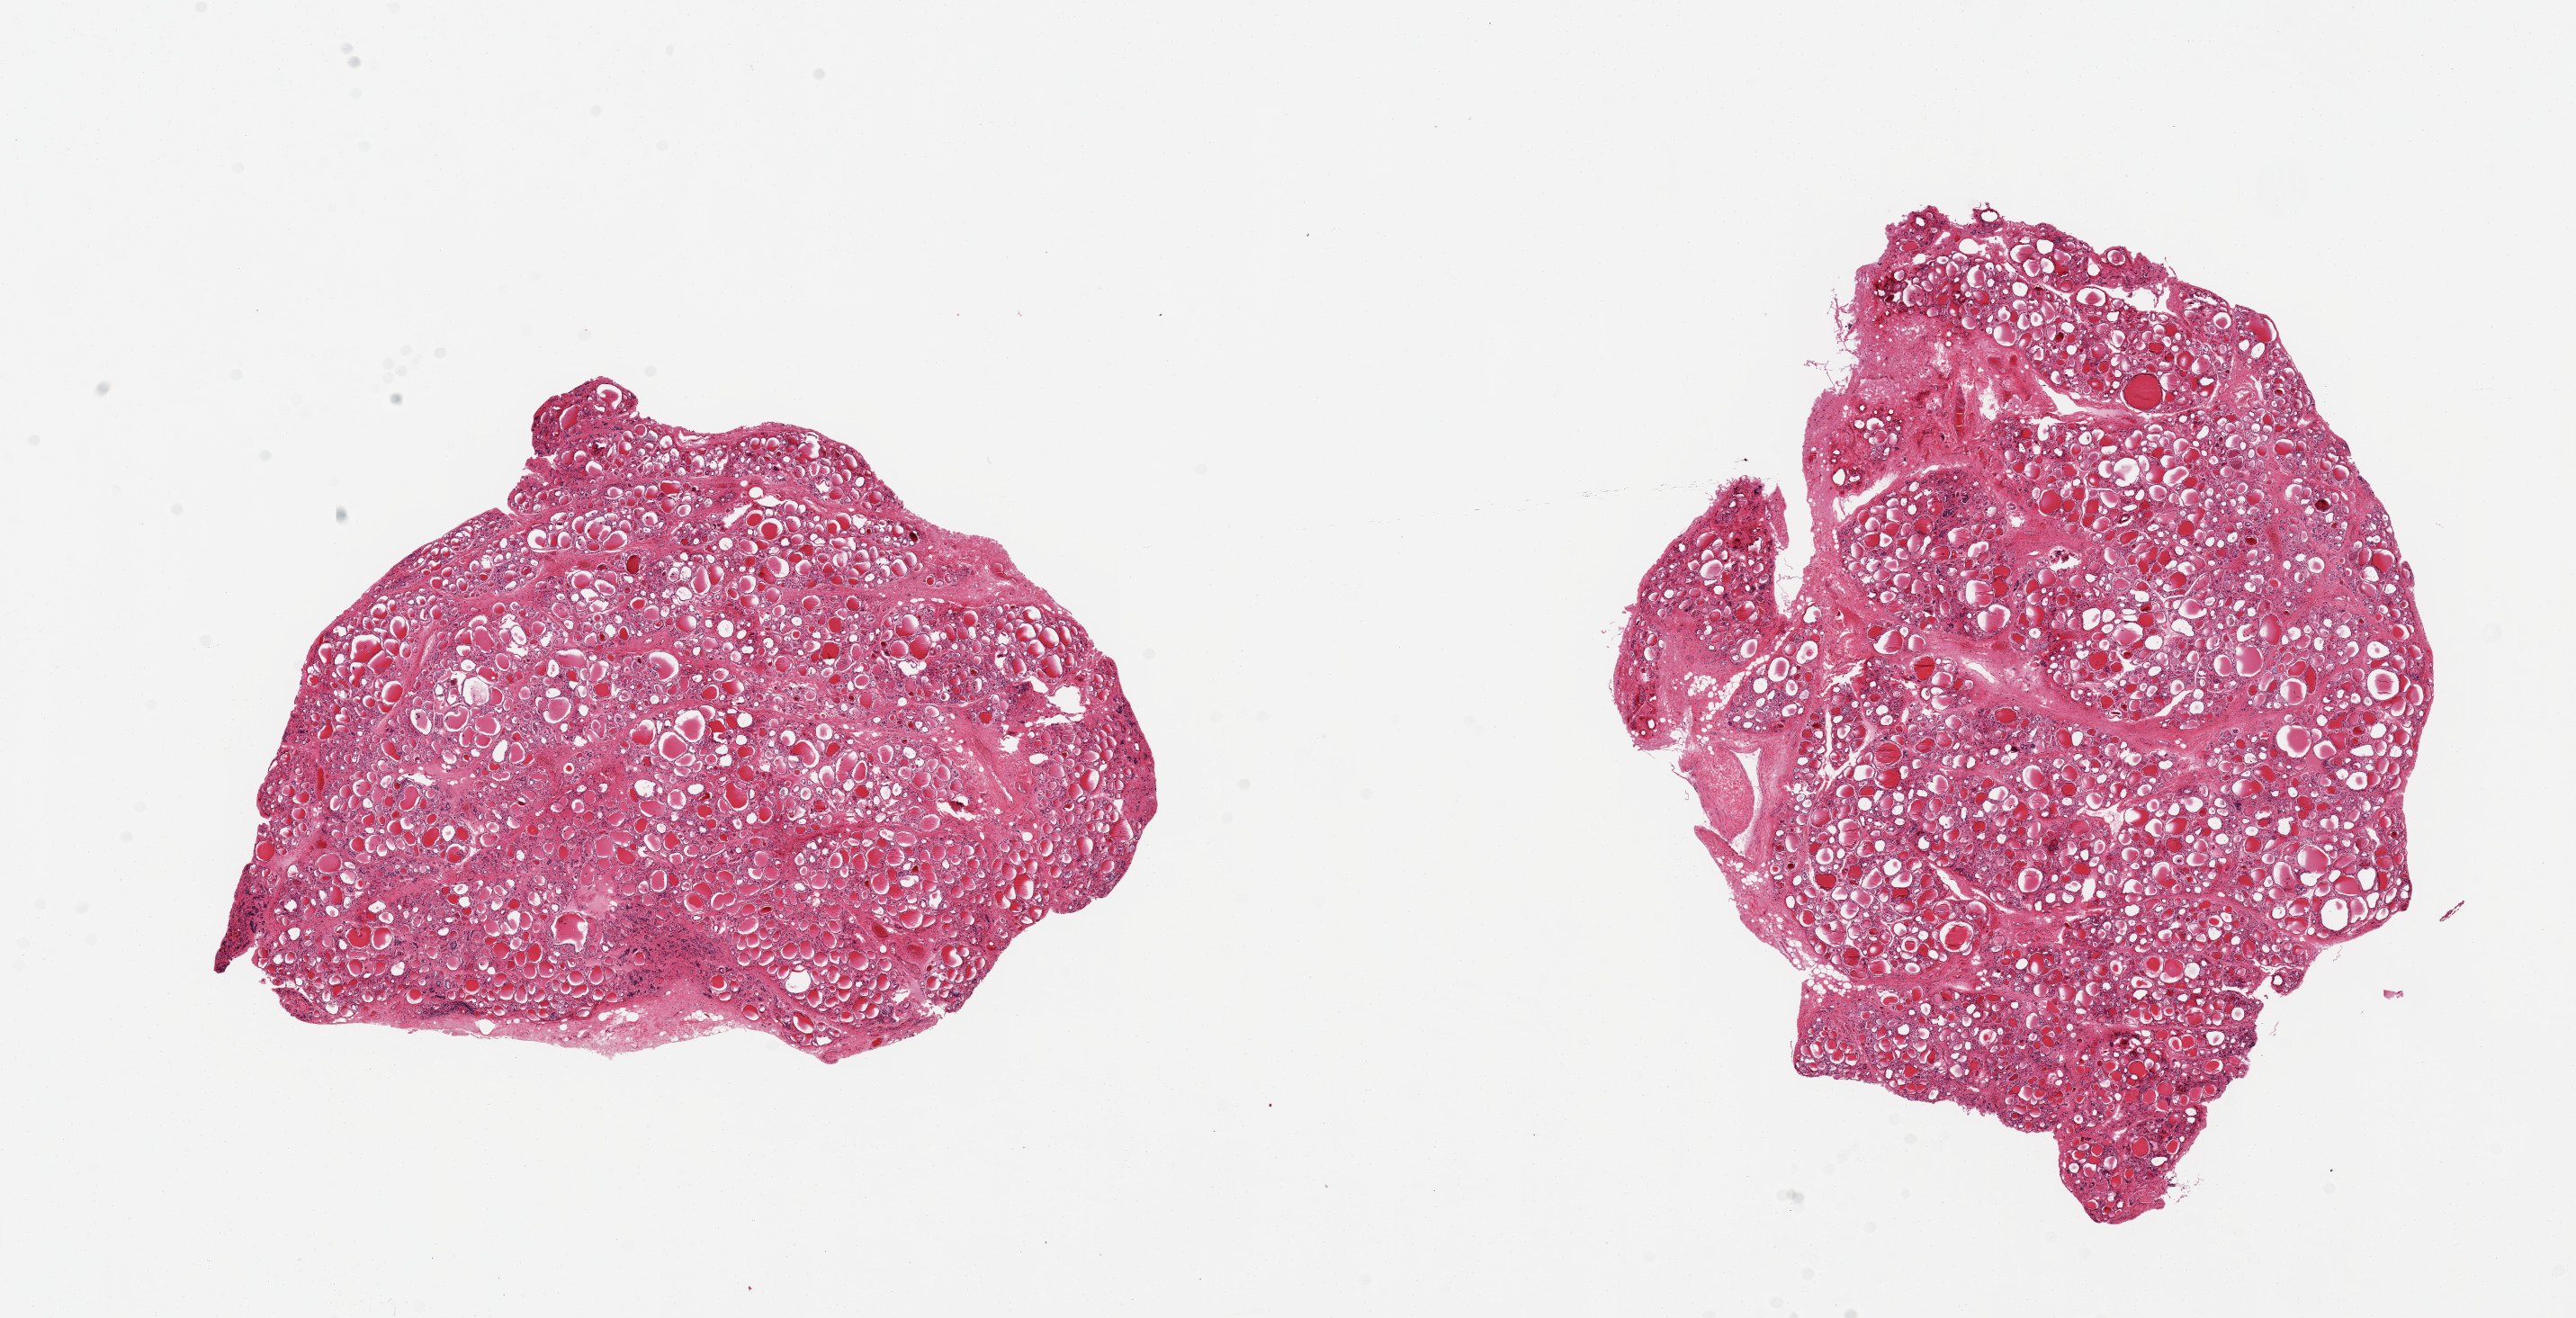
Whole-slide image, hematoxylin and eosin (H&E) stain — low-resolution overview of the scanned area, about 22.6 x 11.6 mm; PAXgene-fixed paraffin-embedded (PFPE) section; section of thyroid (target tissue); tissue donor sample. Female donor.
- reviewer comment on this tissue sample: 2 pieces. 8x6 & 9x7mm; well trimmed